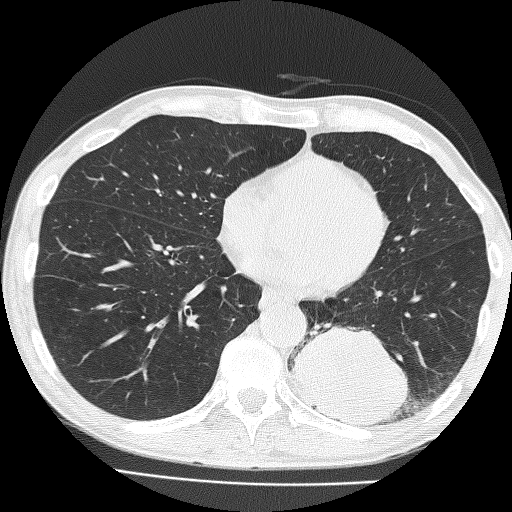
Low-dose screening chest CT, one axial slice; position 64 of 160 along the scan axis; reconstruction kernel FC51; 120 kVp; lung window (W 1500 / L -600 HU); 2 mm slice thickness; 512 × 512 image matrix.
Outlined on this slice (expert manual segmentation):
- lesion 1 (tumor, lower lobe of left lung): bounding box <290,325,410,426> (left, top, right, bottom; pixels)